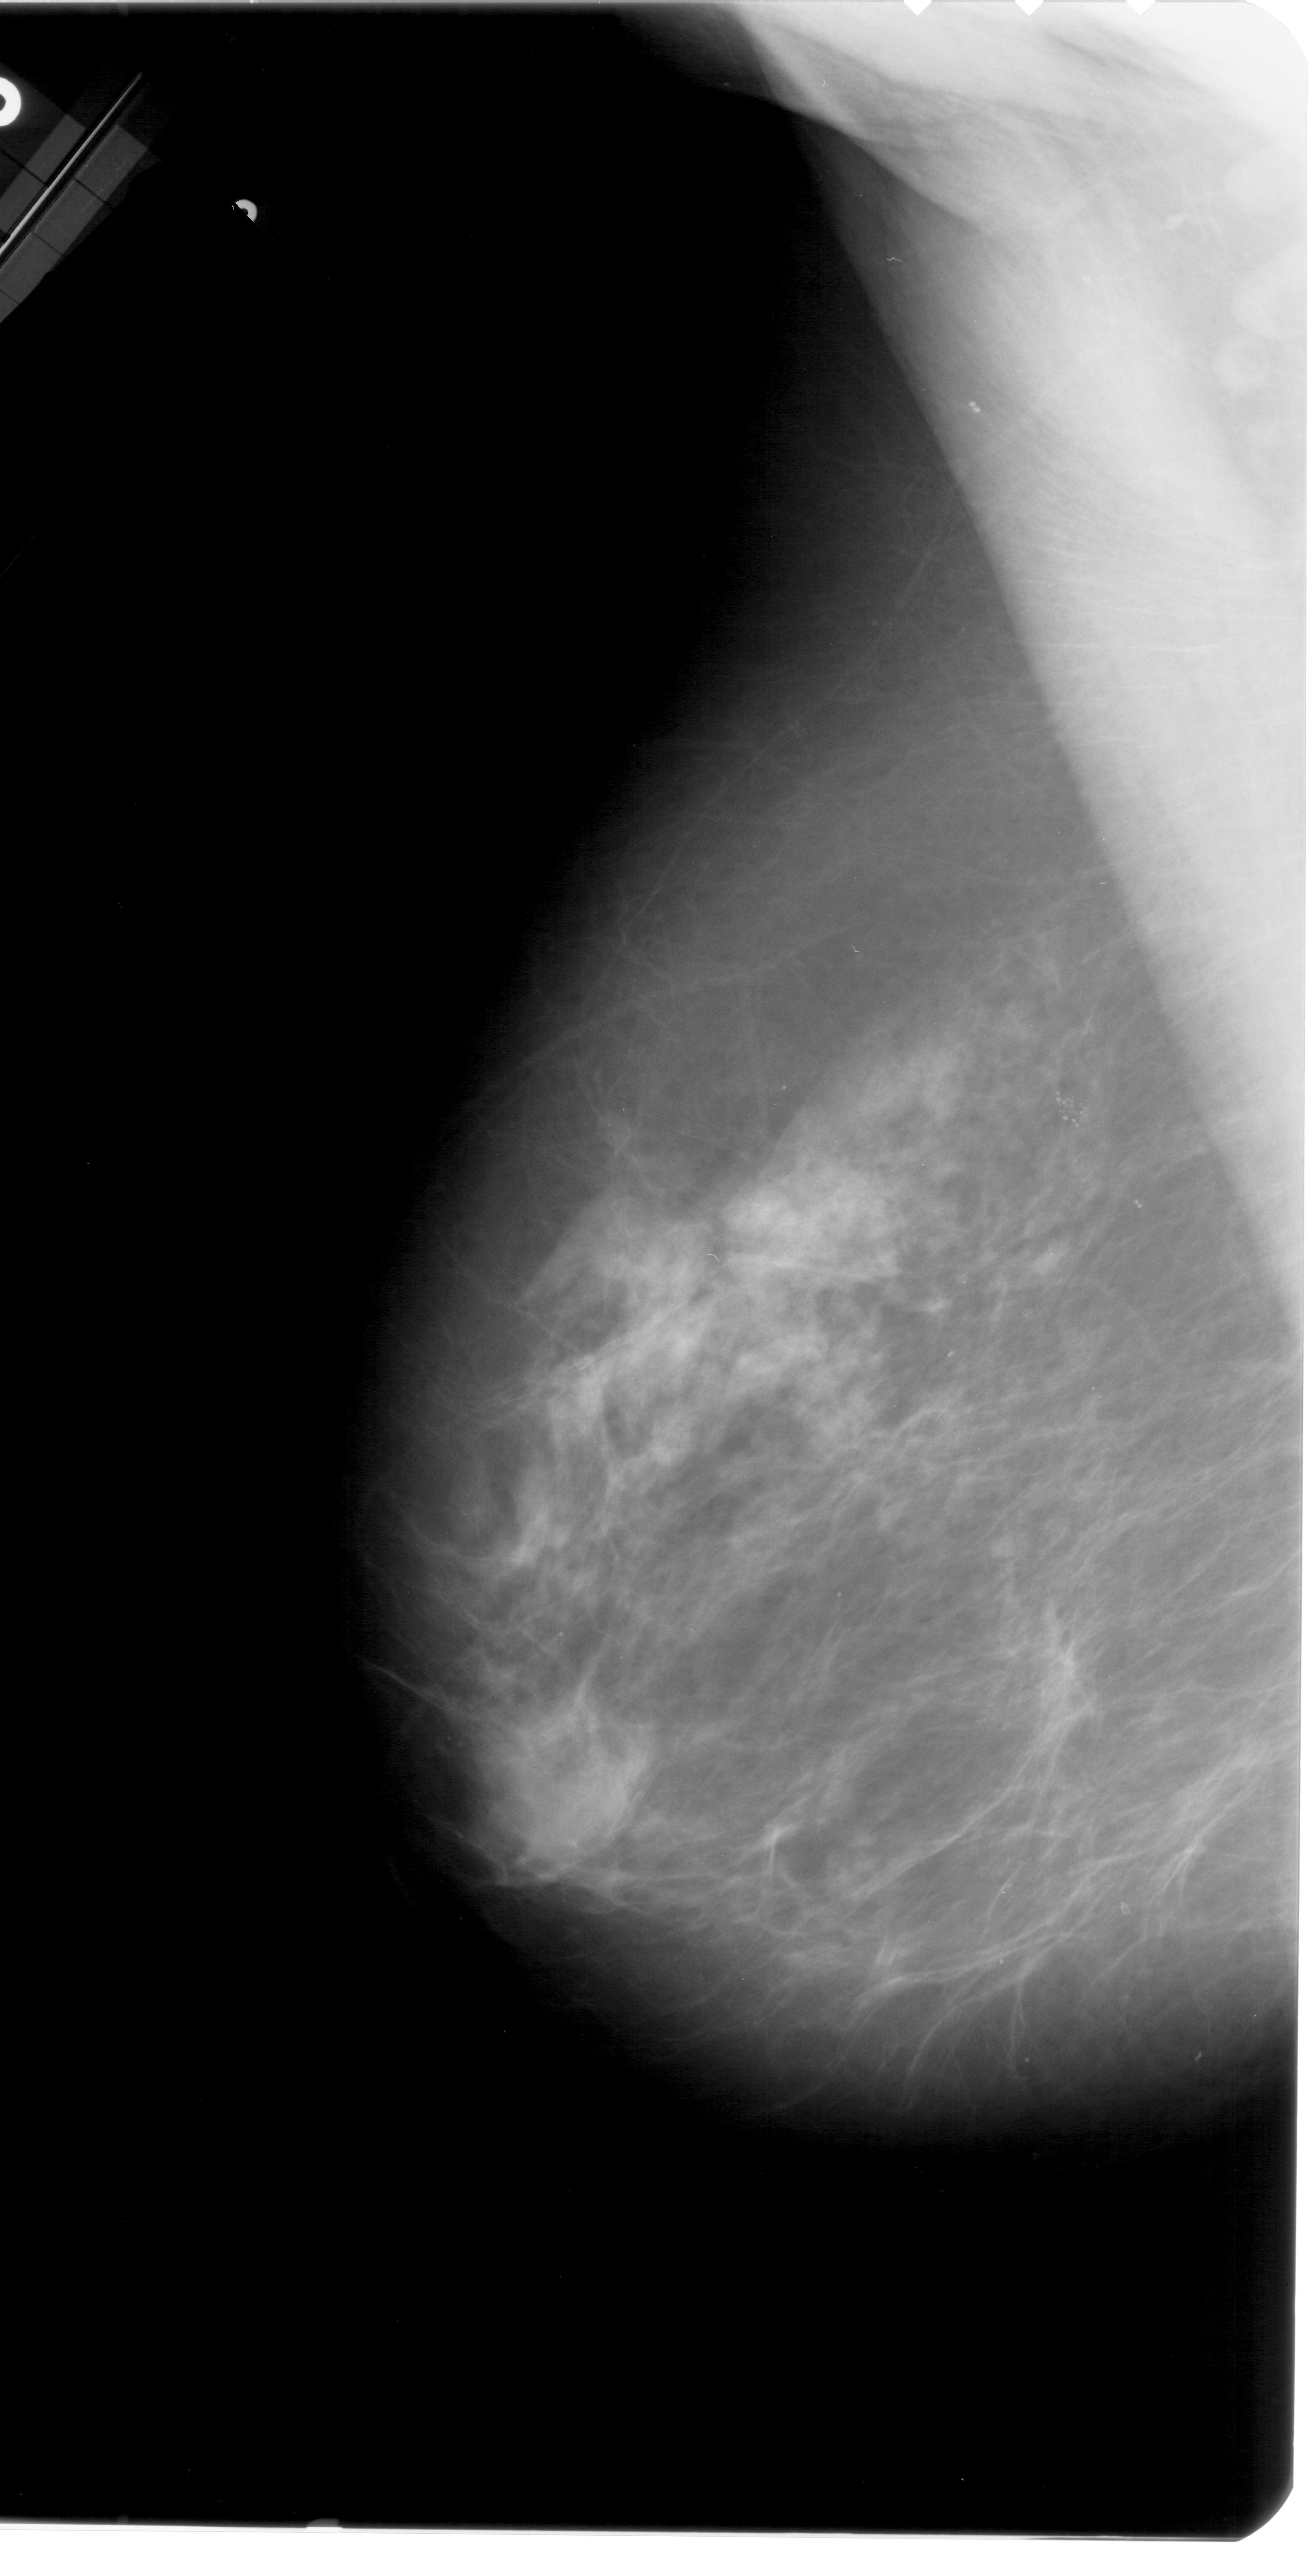
Digitized screen-film mammogram. Left breast. Mediolateral oblique (MLO) view. BI-RADS breast density category 3 (scale 1–4). 1316 × 2576 image matrix.
Marked abnormalities (boxes around the expert regions of interest):
- calcifications, morphology pleomorphic, distribution clustered; BI-RADS assessment category 4; subtlety rating 4 on a 1 (subtle) to 5 (obvious) scale; pathology result (as recorded, not read from the image): malignant: bounding box (x1, y1, x2, y2) in pixels: (1040, 1081, 1104, 1139)